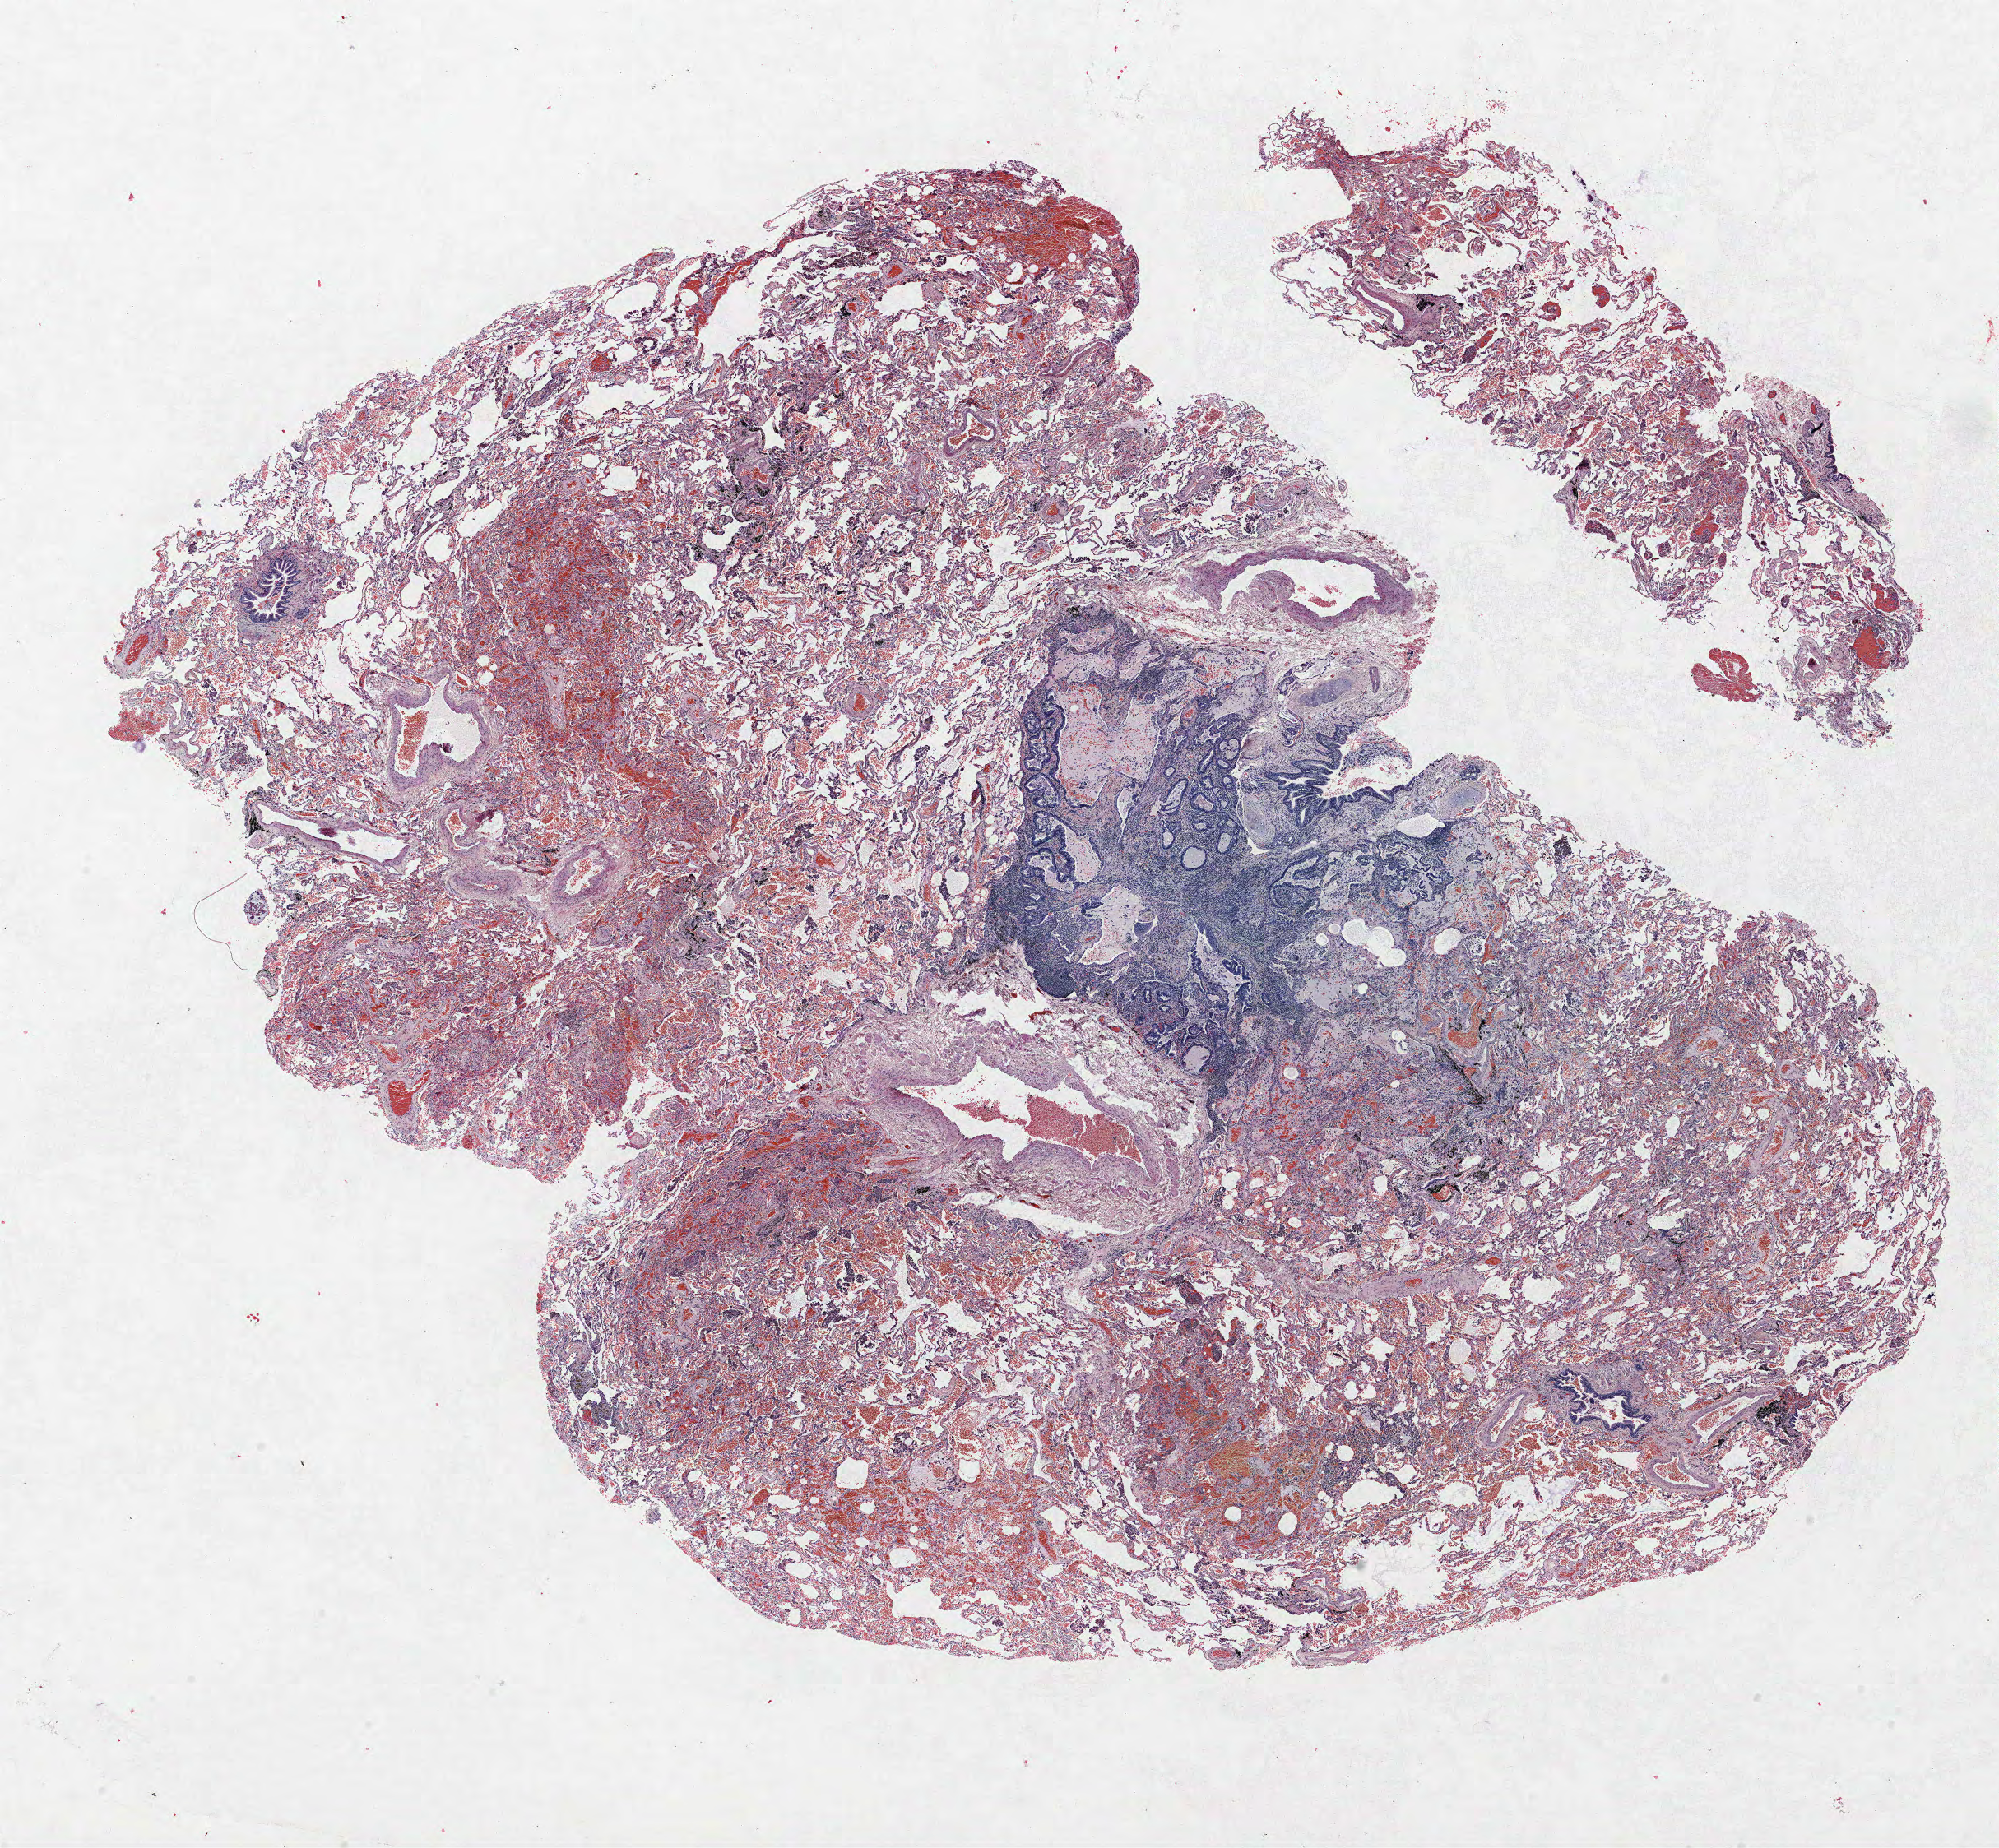
Whole-slide histology image, H&E — low-resolution overview of the scanned area, about 19.4 x 18.0 mm (acquisition: 40x scan). Formalin-fixed paraffin-embedded (FFPE) section. Lung. Male, age 72 at enrolment. Grade: moderately differentiated (G2).
Primary tumour location (clinical record): right upper lobe. Participant's lung-cancer diagnosis: Mucin-producing adenocarcinoma. Tumour size (pathology): 15 mm. Stage (AJCC 6th edition): IA.